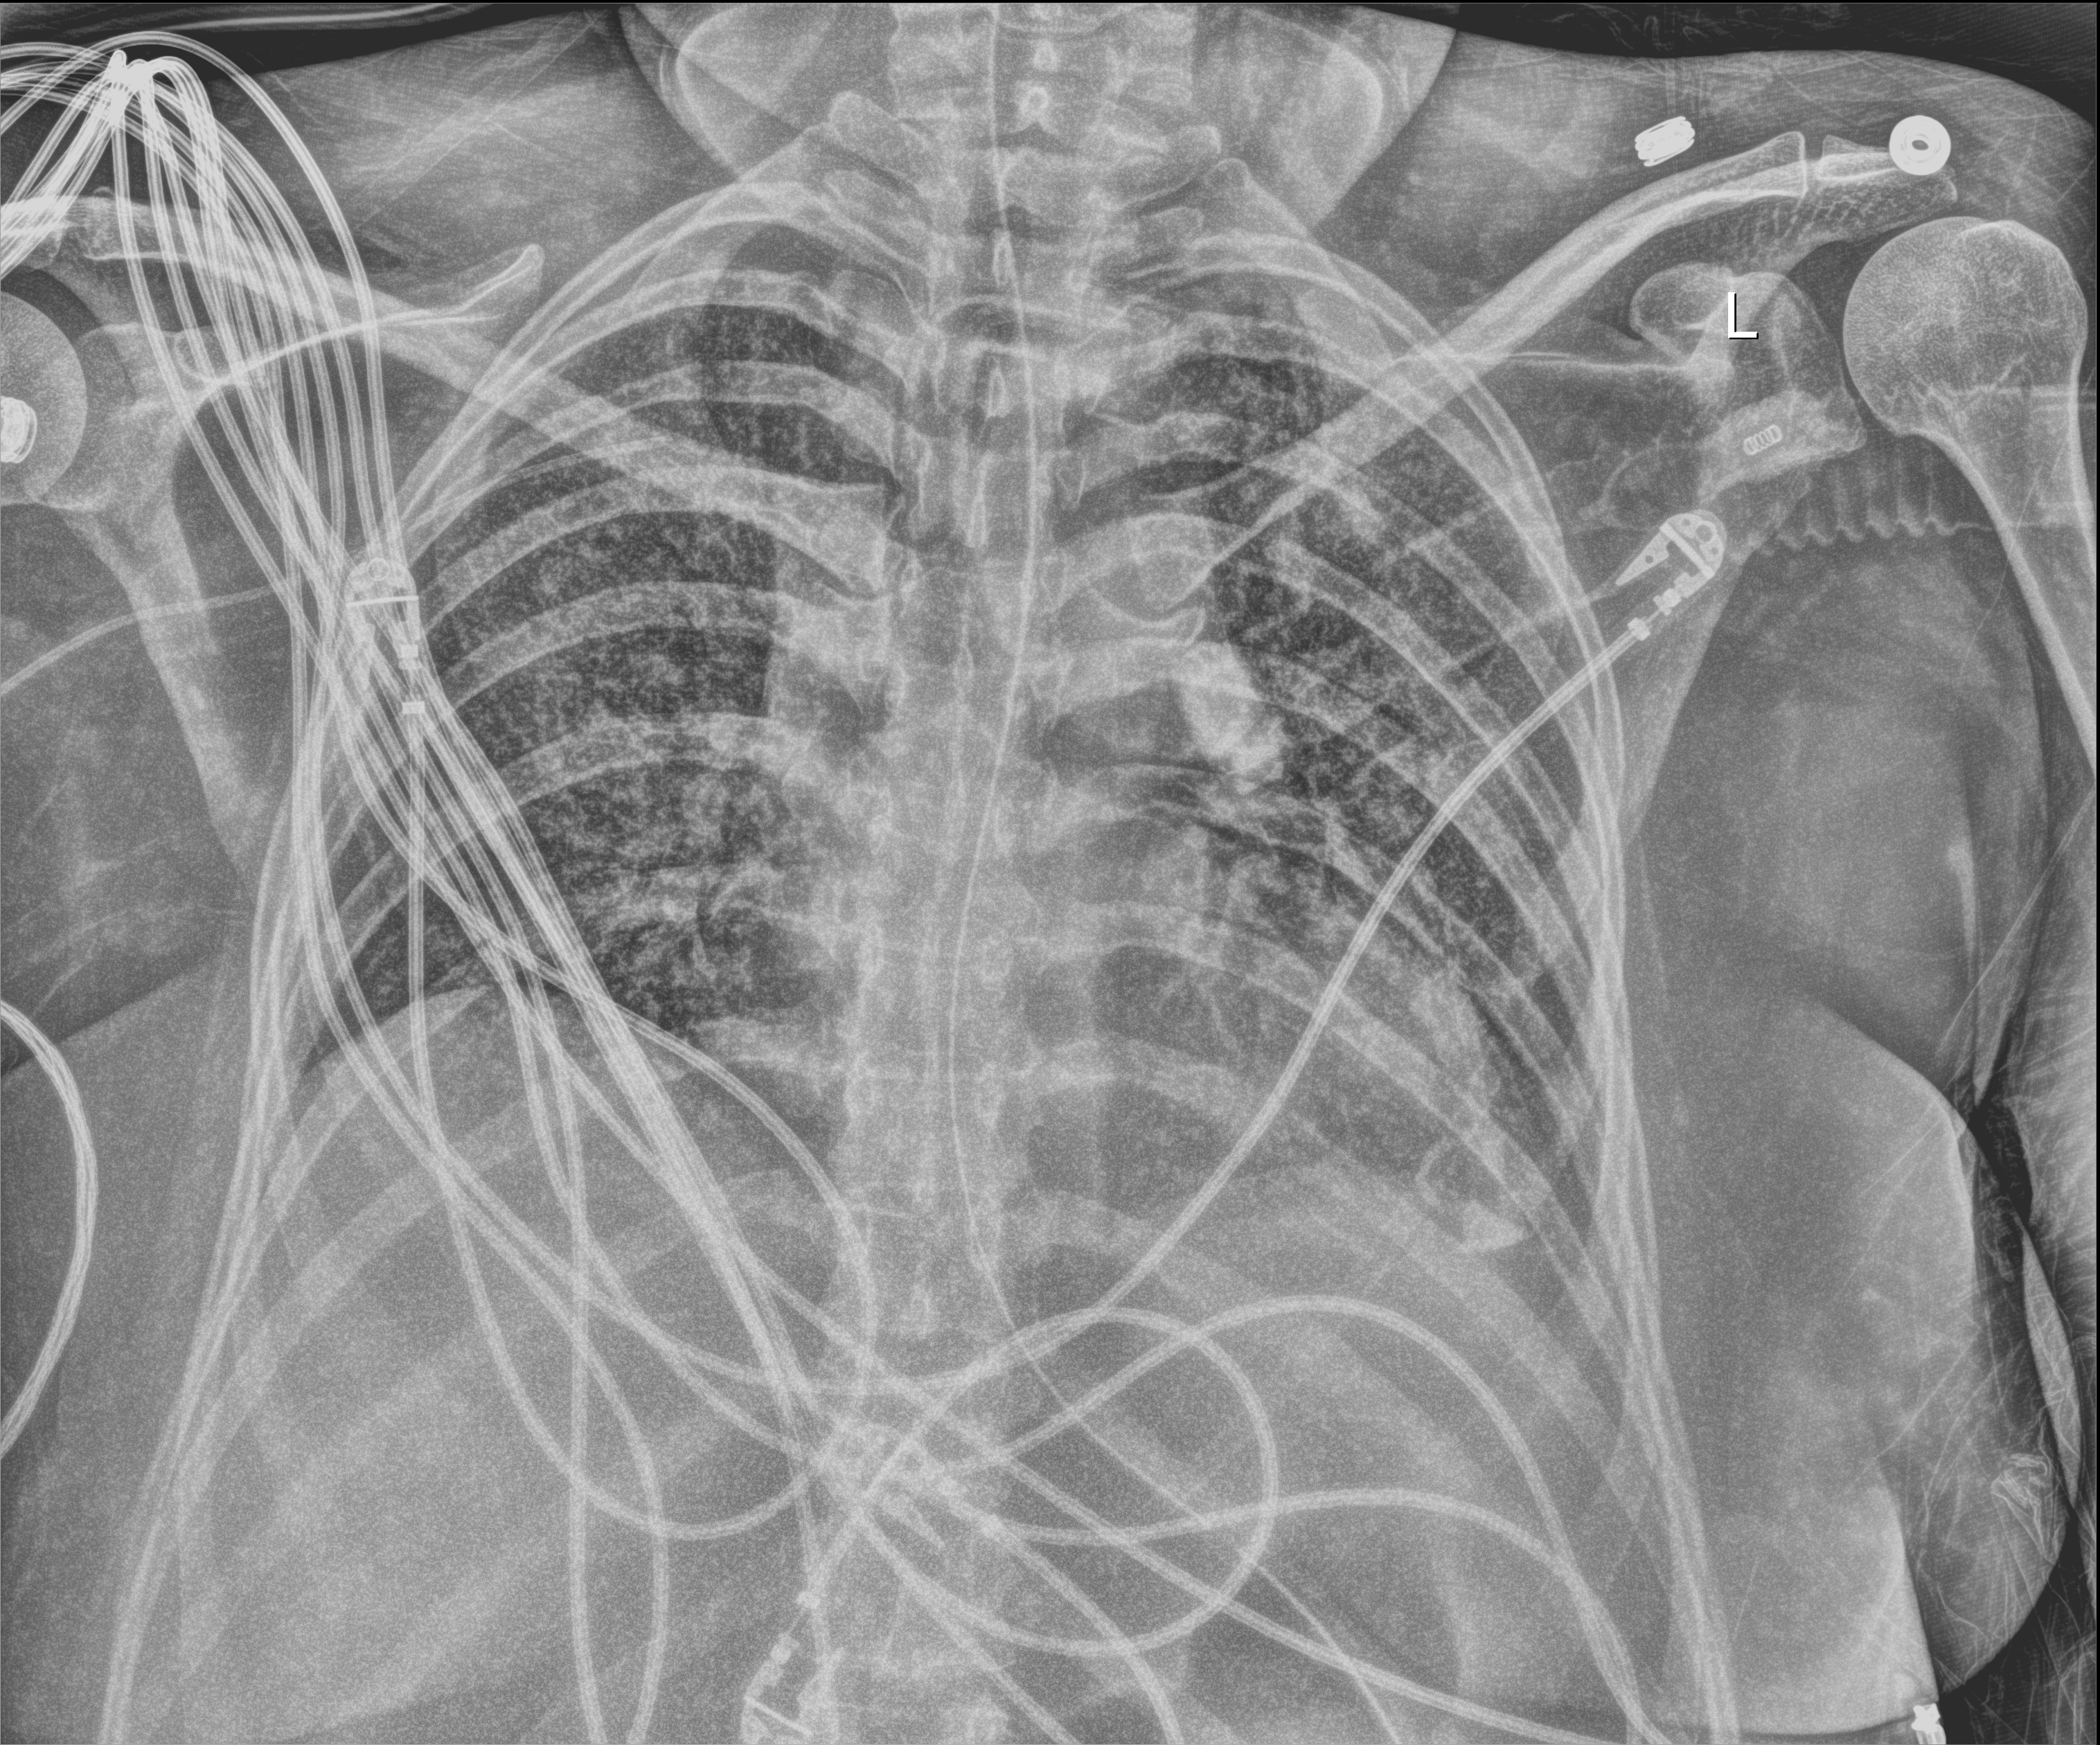
Chest radiograph; anteroposterior (AP) projection. Patient hospitalised with COVID-19; female, aged 18–59 years.
From the hospital-stay record, not from the radiograph (when in the stay this image was taken is not recorded): mechanically ventilated during this hospital stay: yes.